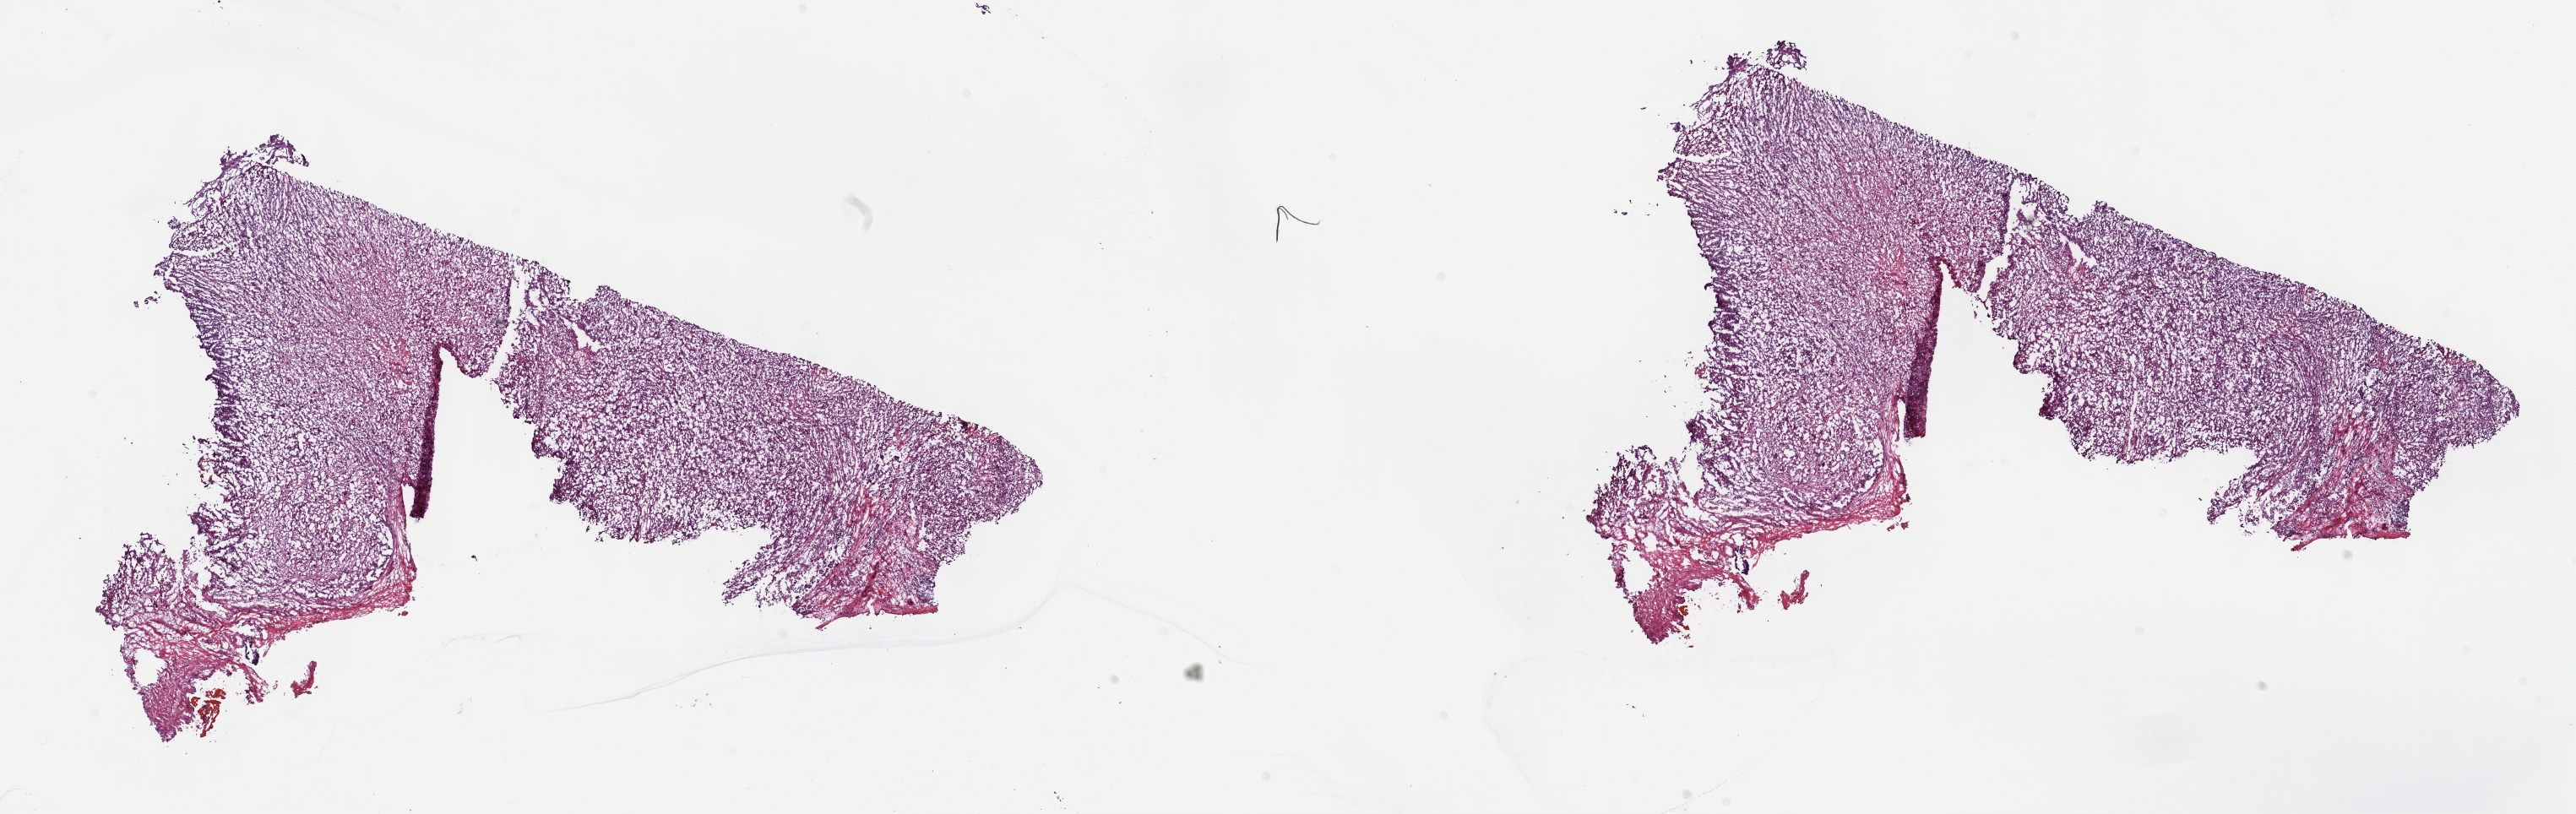
Digitized Hematoxylin and eosin (H&E) stained tissue section (whole slide) — whole scanned area (about 24.7 x 7.8 mm) shown as a low-resolution overview; frozen section; primary tumour sample from the mesothelium. Patient: male, age at initial diagnosis 47 years. Pathologist review of this section (percent, as recorded): tumour cells 100%, tumour nuclei 75%, normal cells 0%, stromal cells 0%, necrosis 0%. Infiltration values recorded for this section: lymphocyte infiltration 3%, monocyte infiltration 0%, neutrophil infiltration 0%.
Diagnosis: Epithelioid mesothelioma, malignant (pleura, NOS). AJCC pathologic stage: II.